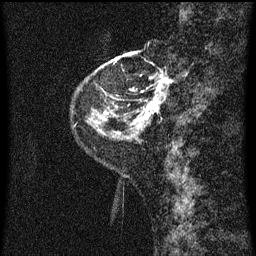
Breast MRI (dynamic contrast-enhanced), one sagittal slice; slice 10 of 60 in the series (ordered by position); dynamic contrast-enhanced series, image 2 of 3 at this slice position (ordered by acquisition); 1.5 T; TE 4.2 ms, TR 8 ms; 2 mm slice thickness; 256 × 256 image matrix. Female patient, age 48 years.
Outlined on this slice (semi-automatically segmented with operator editing):
- analysis volume of interest (the breast-tissue region the enhancement analysis was run in; not a lesion): bounding box [x1, y1, x2, y2] px = [128, 54, 174, 125]
- tumour enhancement mask (voxels above the 70 % enhancement threshold inside the analysis volume of interest): [130, 64, 169, 125]